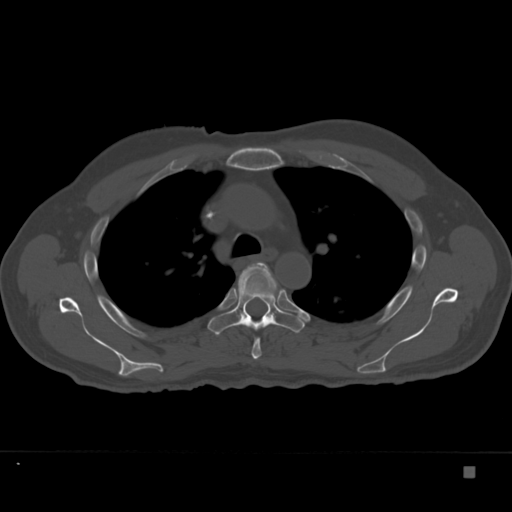
CT including the spine, one axial slice; position 261 of 332 along the scan axis; reconstruction kernel Br40s; 120 kVp; bone window (W 1800 / L 400 HU); 1.5 mm slice thickness; 512 × 512 image matrix, field of view 389 × 389 mm. Male patient, age 72 years. From the clinical record (not read from this slice): primary cancer: skeletal.
Structures marked on this image (semi-automatic segmentation, software-assisted and operator-edited):
- T4 vertebra: bounding box (x1, y1, x2, y2) in pixels: (236, 269, 283, 360)
- T5 vertebra: (208, 262, 305, 335)